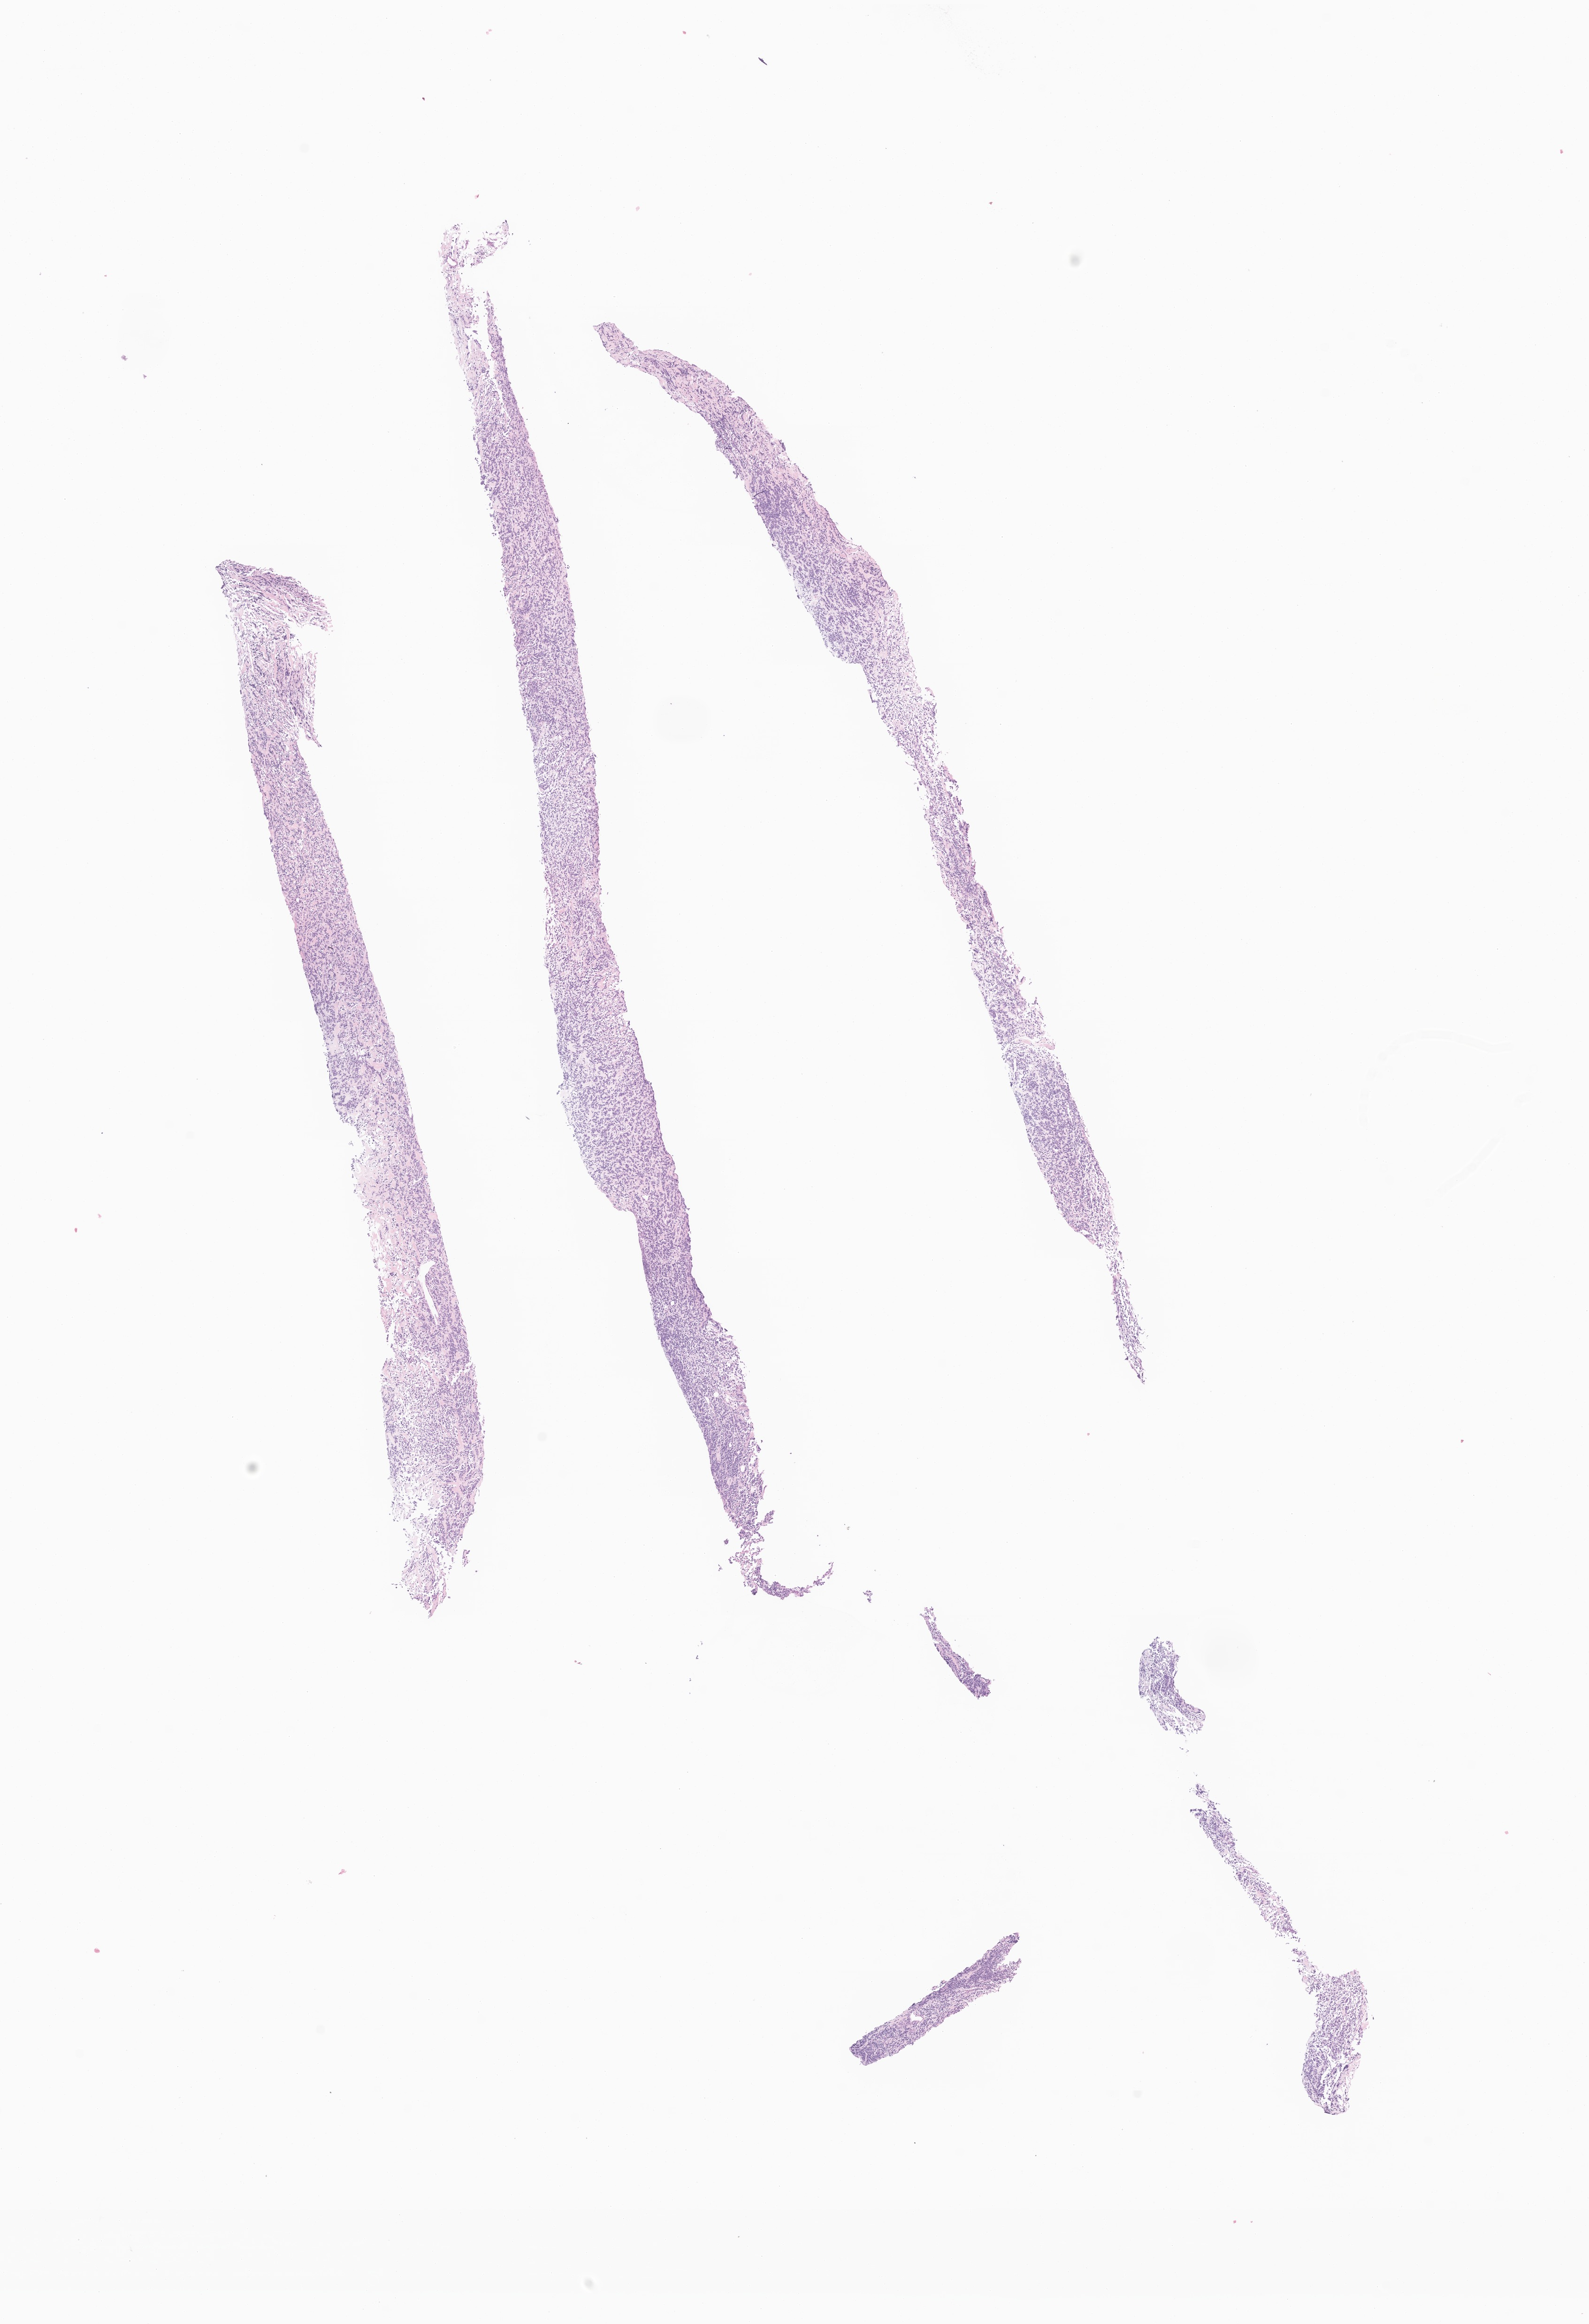
Digitized haematoxylin and eosin-stained section of tumor tissue from the rib, sternum and/or clavicle — a low-resolution overview of the entire scanned area, about 14.3 x 20.9 mm. Formalin-fixed paraffin-embedded section. Patient male; age 130 months (10 years 10 months).
• recorded diagnosis: Sarcoma, NOS